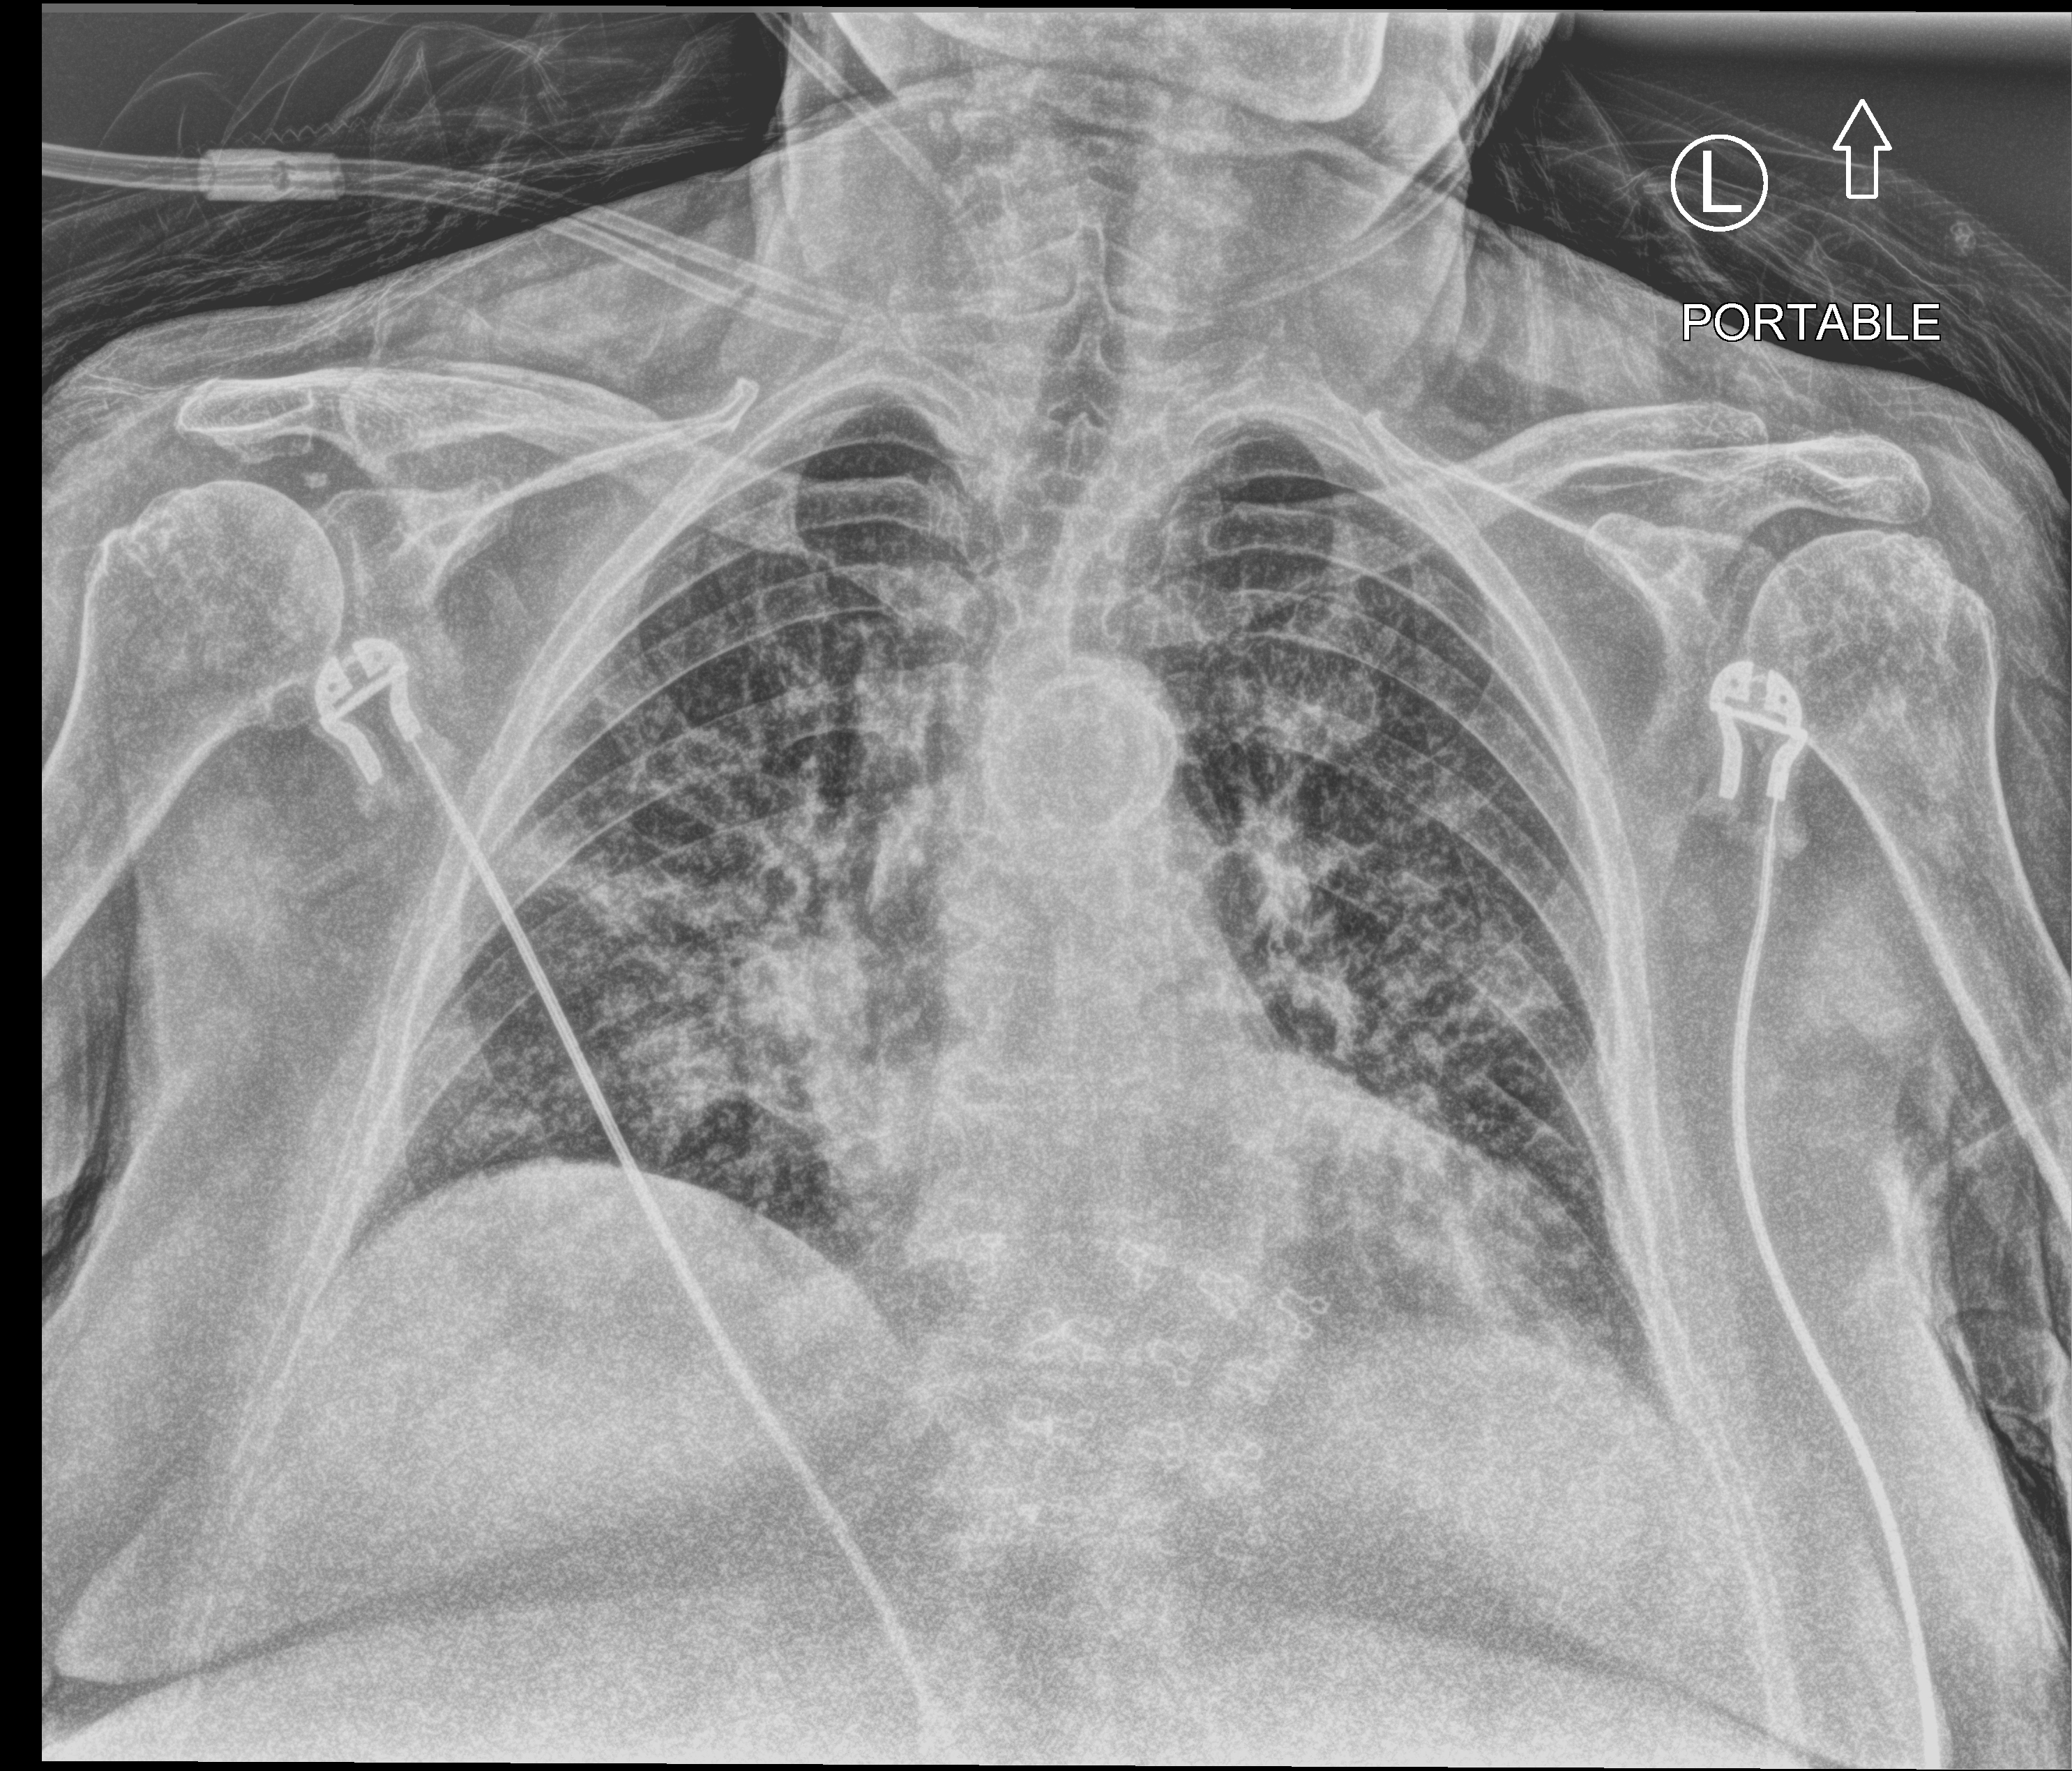
Chest X-ray (portable), anteroposterior (AP) projection. Female patient hospitalised with COVID-19, age 75–90 years.
Hospital-stay facts (about this admission, not read from this image; timing relative to this image not recorded): chronic kidney disease (admission record): no.